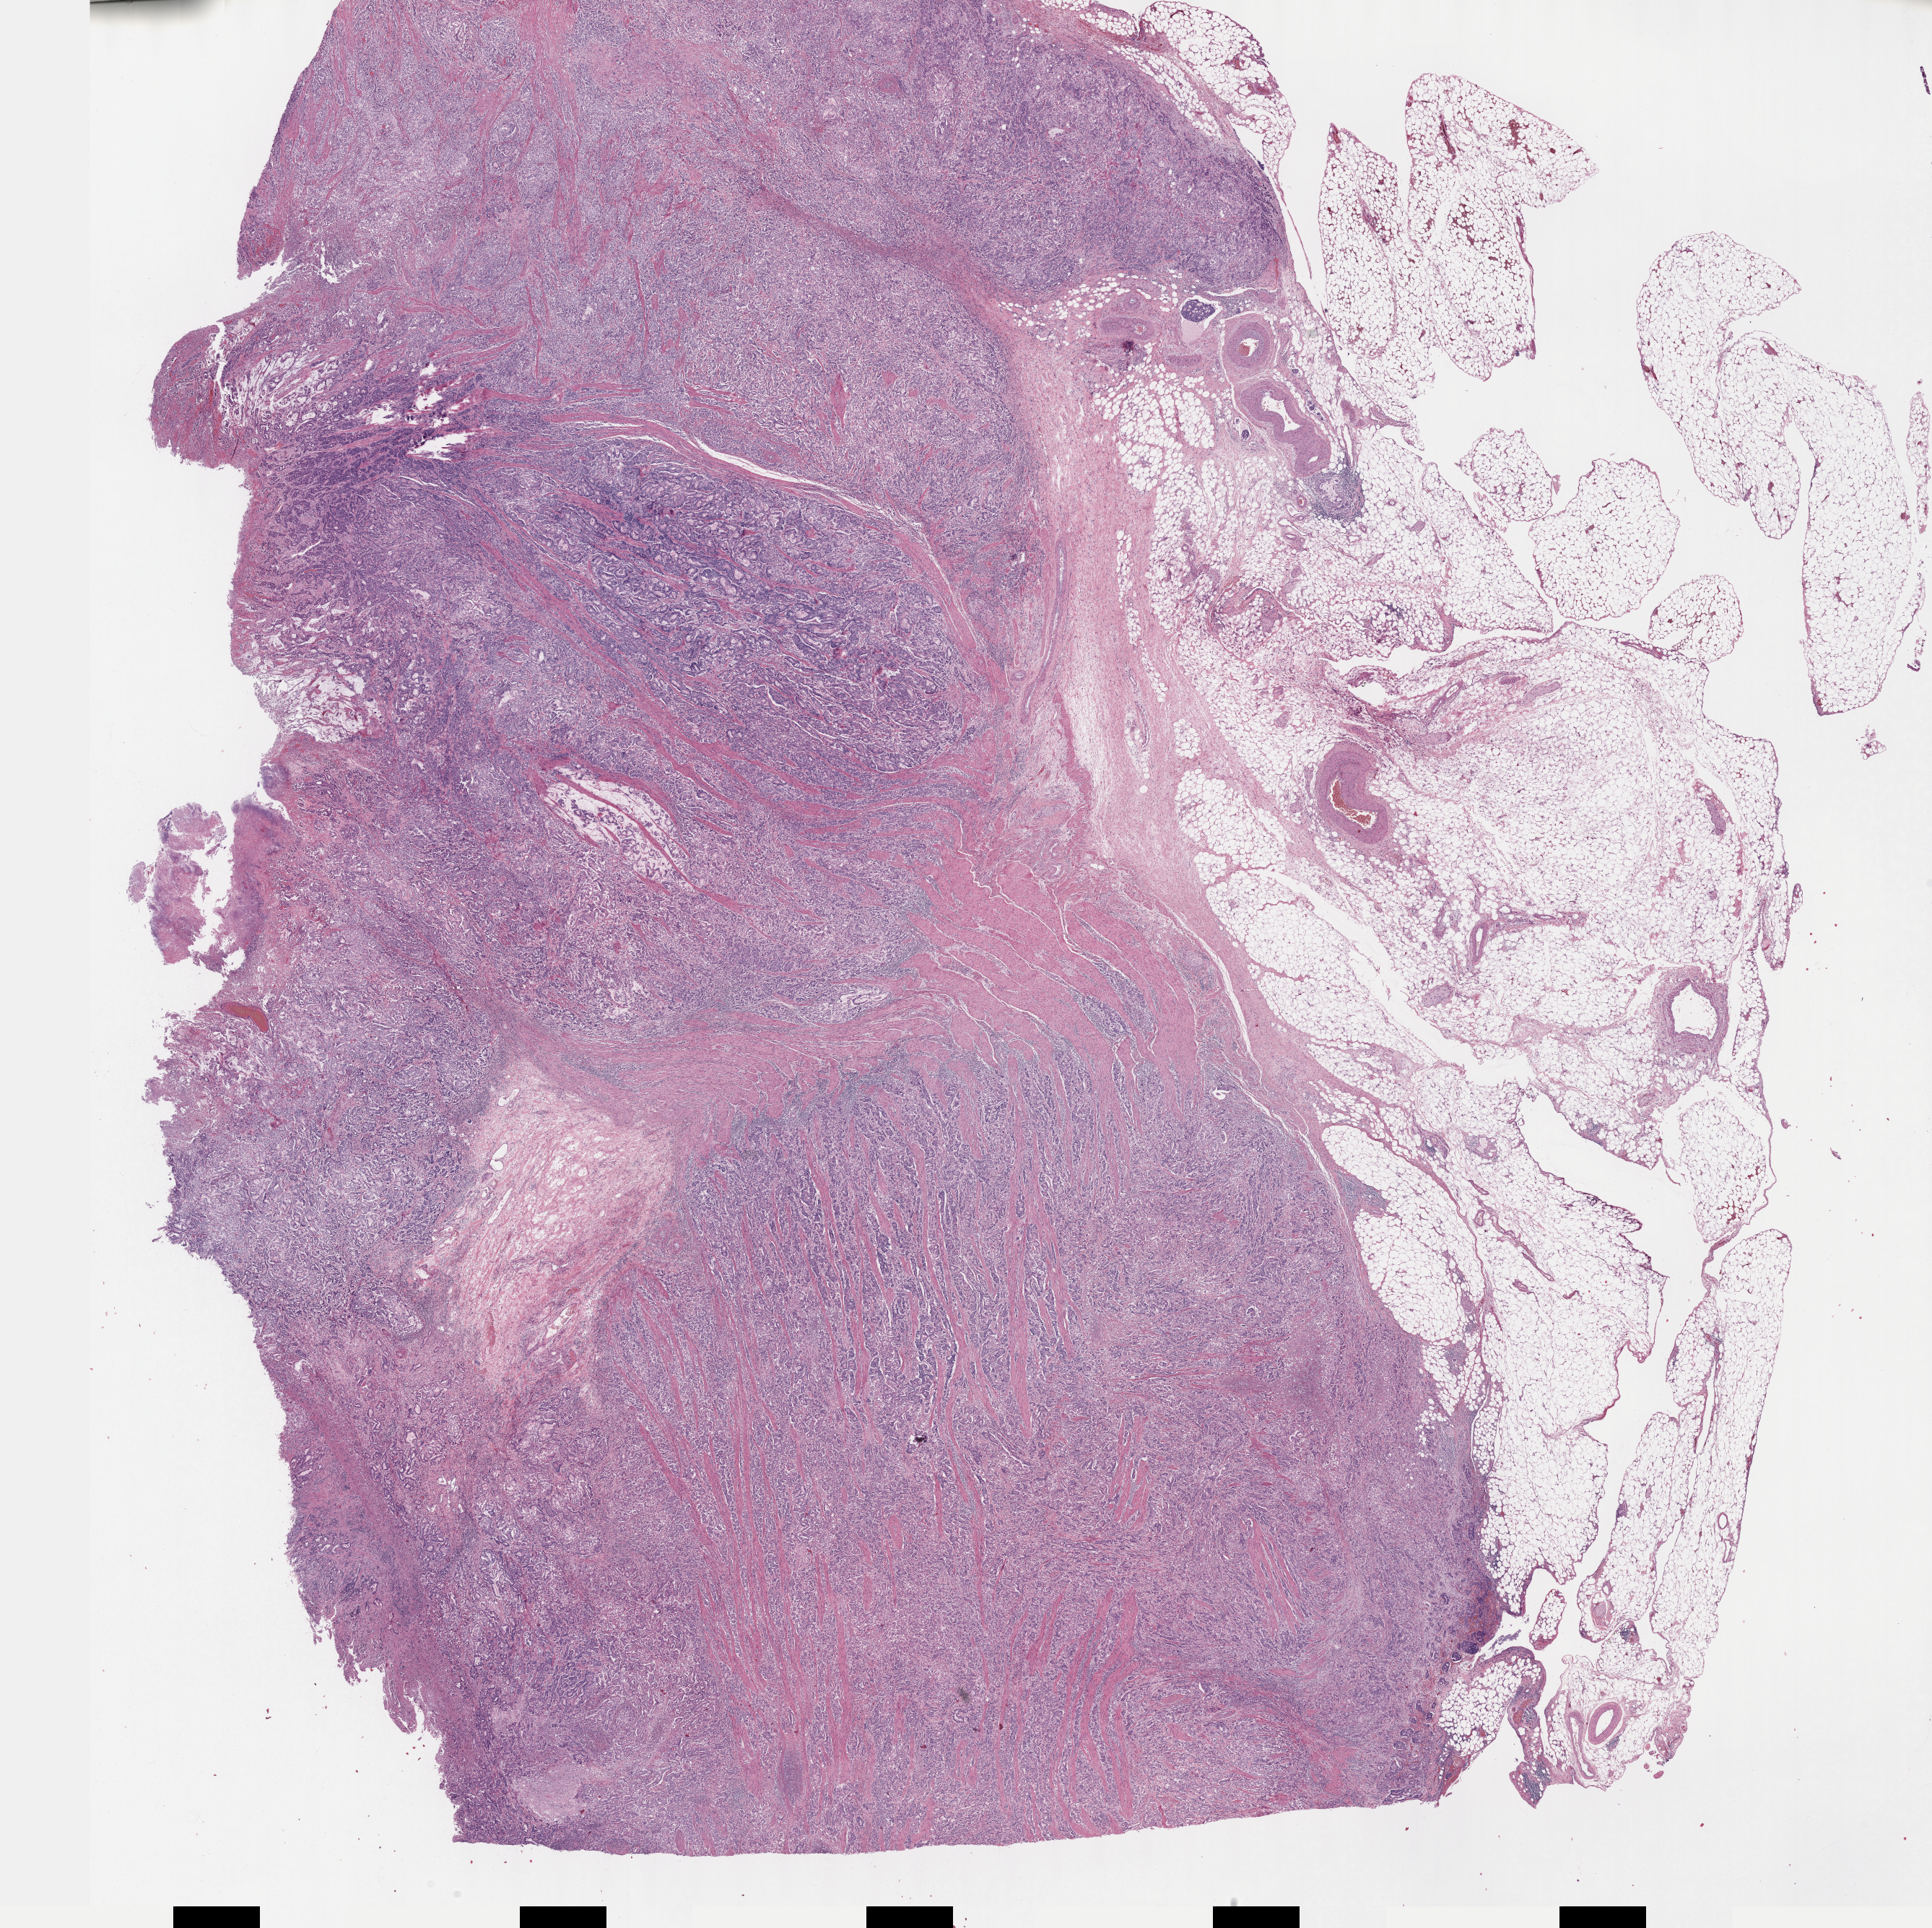
Digitized H&E tissue section (whole slide) — a low-resolution overview of the entire scanned area, about 21.6 x 21.6 mm; formalin-fixed paraffin-embedded (FFPE) diagnostic section; sample: primary tumour, stomach. Male, age 70 years at initial diagnosis. Histologic grade: G2 (moderately differentiated).
Lymph nodes positive (case pathology): 5 of 33 examined. AJCC pathologic stage: IIIC. Histologic diagnosis: Adenocarcinoma, intestinal type (body of stomach).